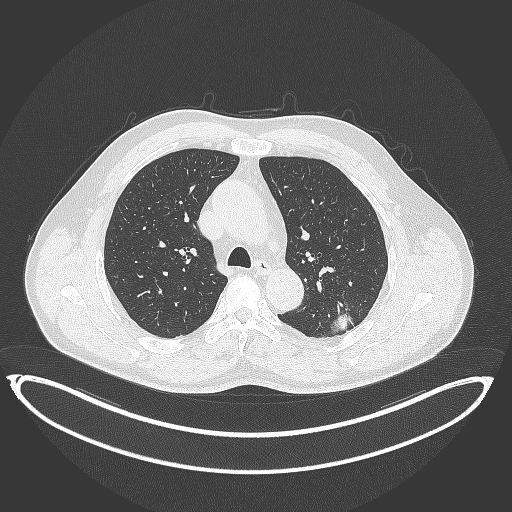
Chest CT, one axial slice. Slice 248 of 399 in the series (ordered by position). Reconstruction kernel B70f. 120 kVp. Lung window (W 1500 / L -600 HU). 1 mm slice thickness. 512 × 512 image matrix, field of view 469 × 469 mm. Male patient, age 58 years. From the clinical record (not read from this slice): clinical TNM (as recorded): T1c N0 M0.
Structures marked on this image (bounding box drawn by a radiologist):
- lung tumour (recorded histology: adenocarcinoma): bounding box (x1, y1, x2, y2) in pixels: (330, 303, 359, 337)